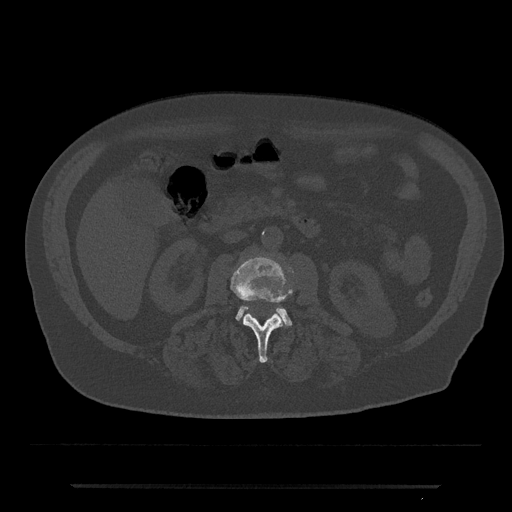
CT including the spine, one axial slice; position 450 of 797 along the scan axis; reconstruction kernel Br40s/3; 120 kVp; bone window (W 1800 / L 400 HU); 0.5 mm slice thickness; 512 × 512 image matrix. Patient: male, 80 years. From the clinical record (not read from this slice): primary cancer: prostate.
Outlined on this slice (semi-automatically segmented with operator editing):
- L2 vertebra: bounding box <231,256,292,363> (left, top, right, bottom; pixels)
- L3 vertebra: <236,306,292,326>